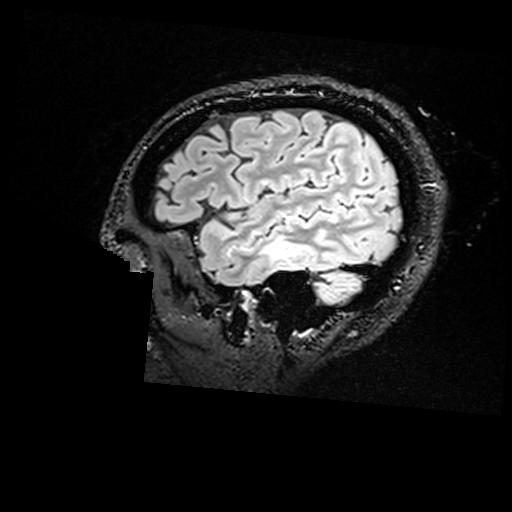
Brain MRI from a brain-tumour surgery series, one sagittal slice; position 132 of 176 along the scan axis; T2 FLAIR; 1 mm slice thickness; 512 × 512 image matrix, field of view 250 × 250 mm. Case-level facts recorded for this patient, not image findings: histopathology: Non-tumor destructive chronic inflammatory lesion with abnormal vasculature.
Structures marked on this image (outlined manually by an expert reader):
- residual tumour: bounding box <280,241,295,257> (left, top, right, bottom; pixels)